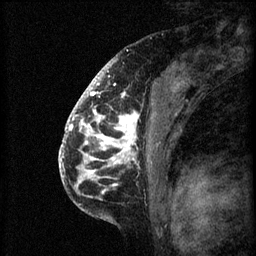
Breast MRI (dynamic contrast-enhanced), one sagittal slice; 3 images stored at this slice position (order not interpretable as contrast timing); 1.5 T; TE 4.2 ms, TR 8.2 ms; 256 × 256 image matrix. Female patient, age 41 years.
Structures marked on this image (semi-automatic segmentation, software-assisted and operator-edited):
- analysis volume of interest (the breast-tissue region the enhancement analysis was run in; not a lesion): box from (x=72, y=108) to (x=157, y=205) px
- tumour enhancement mask (voxels above the 70 % enhancement threshold inside the analysis volume of interest): (x=72, y=108)–(x=140, y=187)